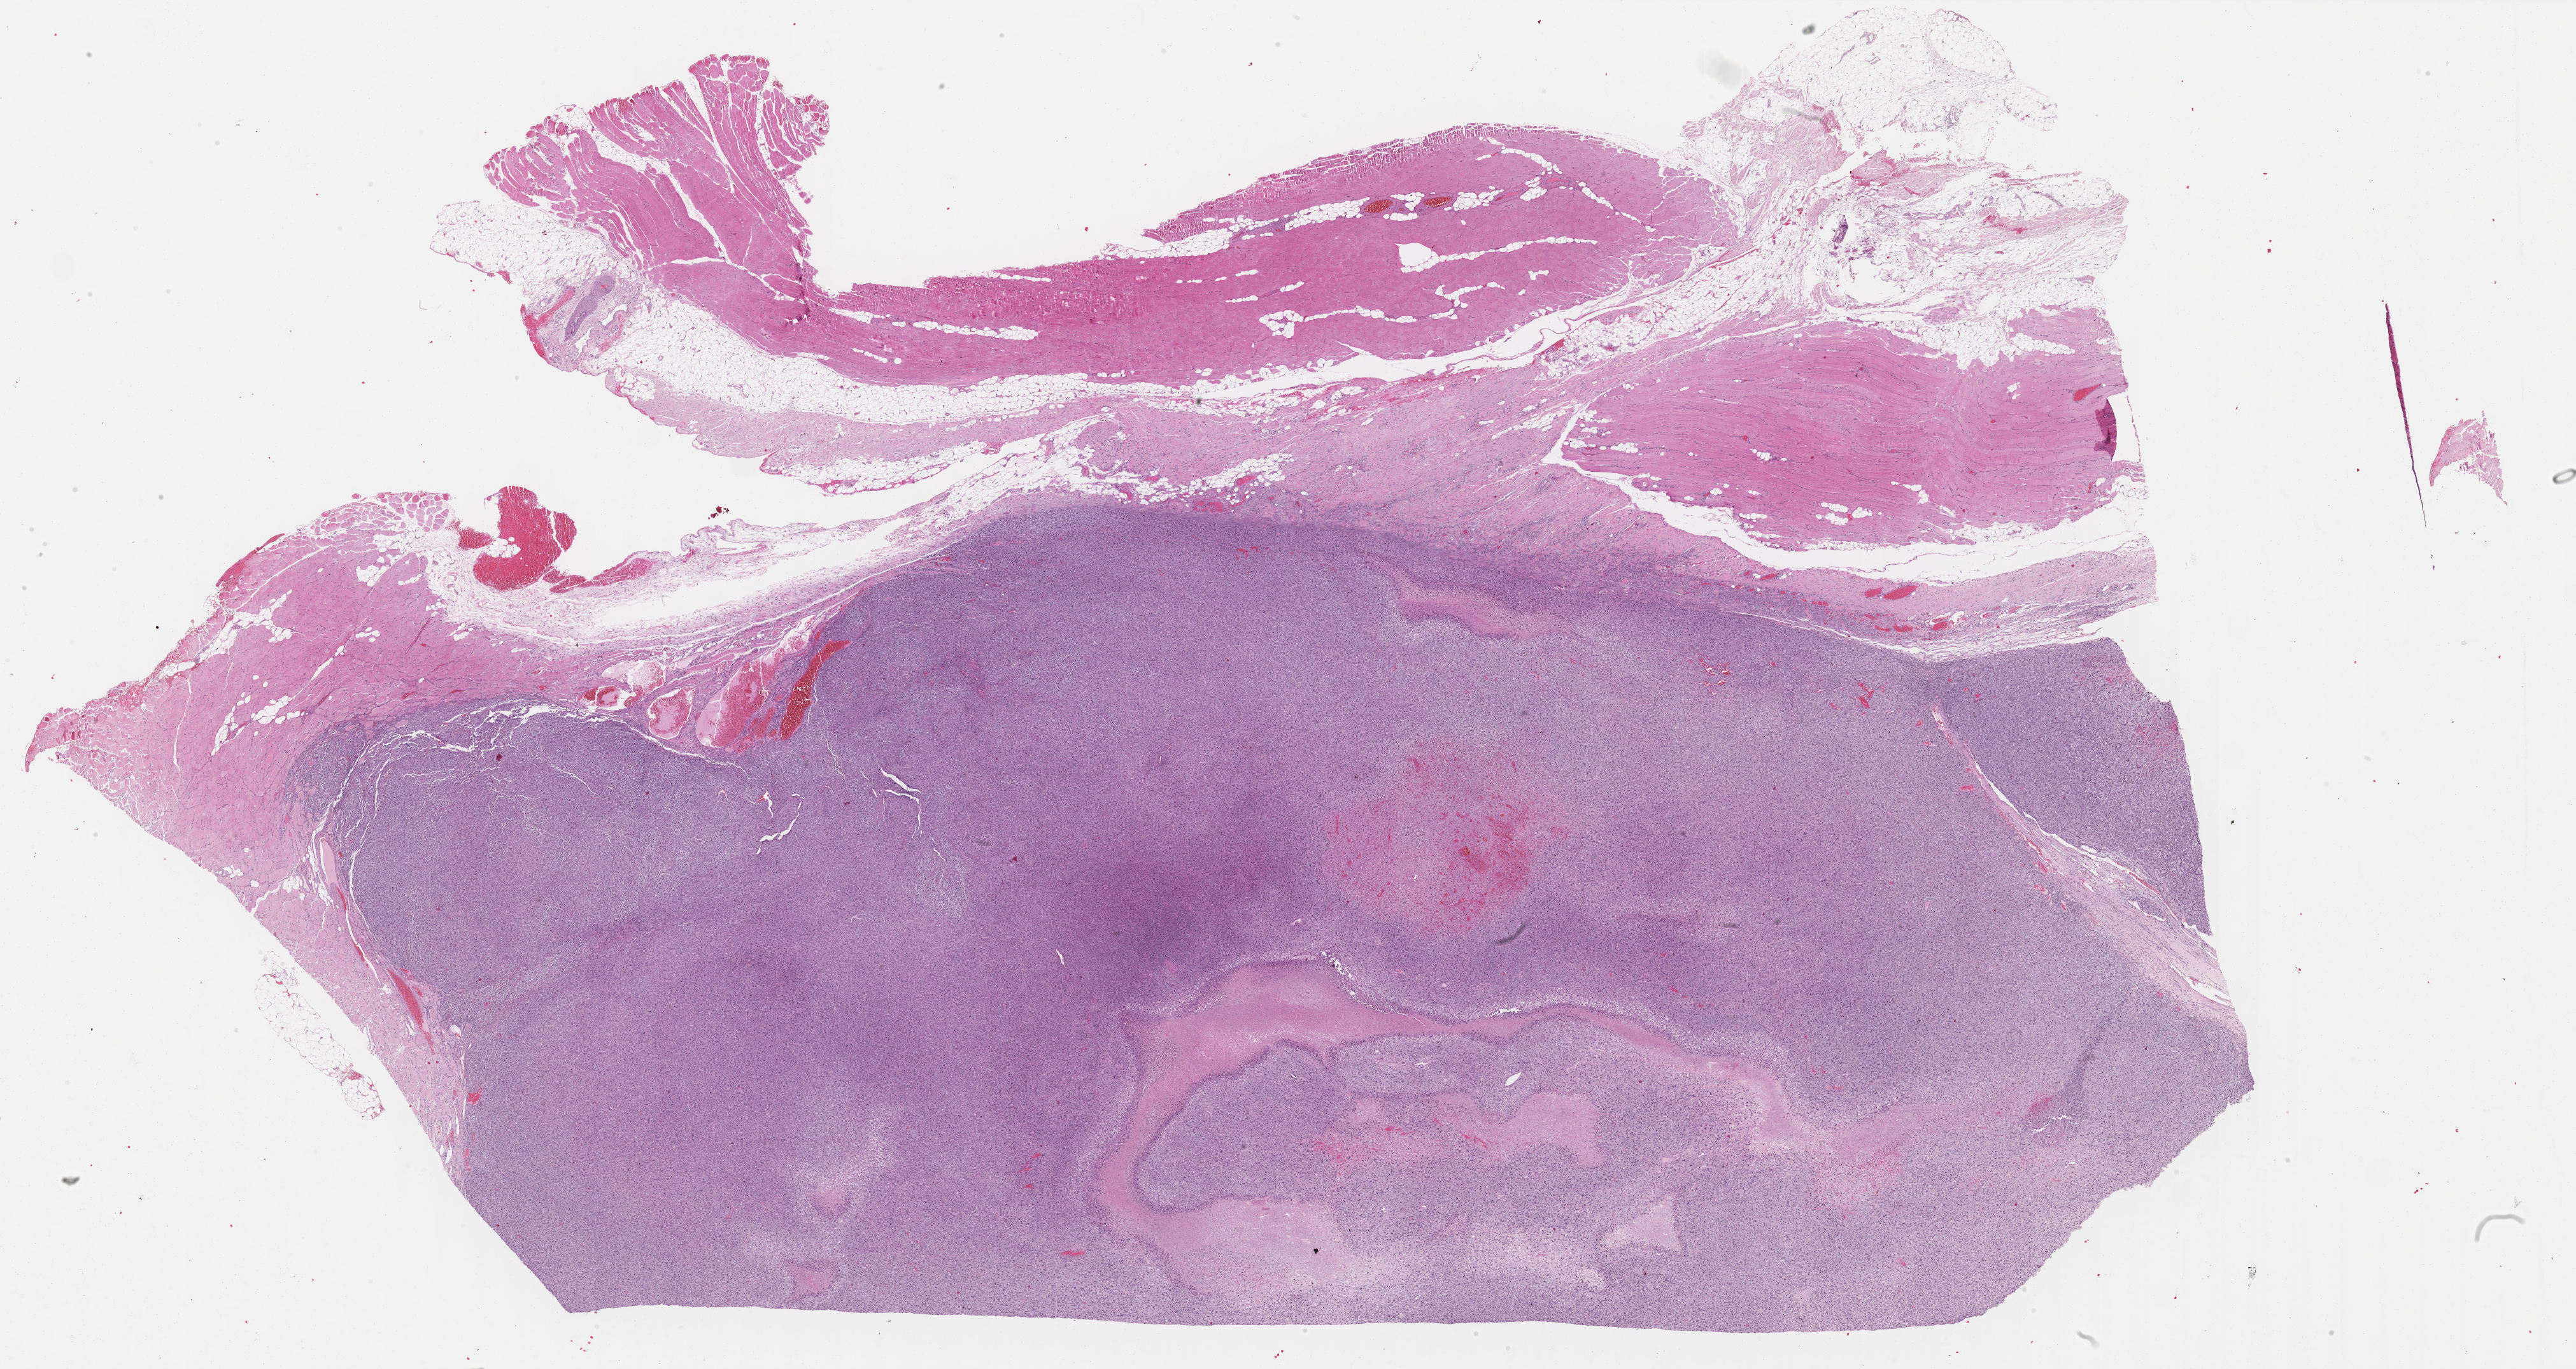
Digitized Hematoxylin and eosin (H&E) stained tissue section (whole slide) — a low-resolution overview of the entire scanned area, about 32.7 x 17.4 mm (acquisition: 40x scan); FFPE section; connective, subcutaneous and other soft tissues, primary tumour sample. Female patient; age at initial diagnosis 86 years.
Histologic diagnosis: Fibromyxosarcoma (connective, subcutaneous and other soft tissues of pelvis).